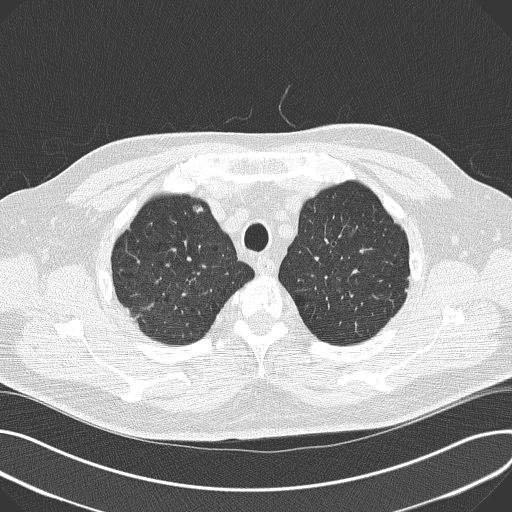
Axial slice from a low-dose chest CT screening exam. Third screening round (two years after baseline). Lung window (W 1500 / L -600 HU). 2 mm slice thickness. 120 kVp. 512 × 512 image matrix. Male participant, aged 68 years at enrolment. Current smoker at enrolment.
Expert-annotated lung lesion, box from (x=179, y=192) to (x=216, y=226) px. The screening reader recorded 3 non-calcified nodules or masses ≥4 mm on this exam (right upper lobe, left lower lobe, right lower lobe); which of them this box marks is not recorded. Later outcome: lung cancer diagnosed 95 days after this screen — combined small cell carcinoma, right upper lobe, undifferentiated (G4), stage IIIB (AJCC 6th edition), 30 mm at pathology.